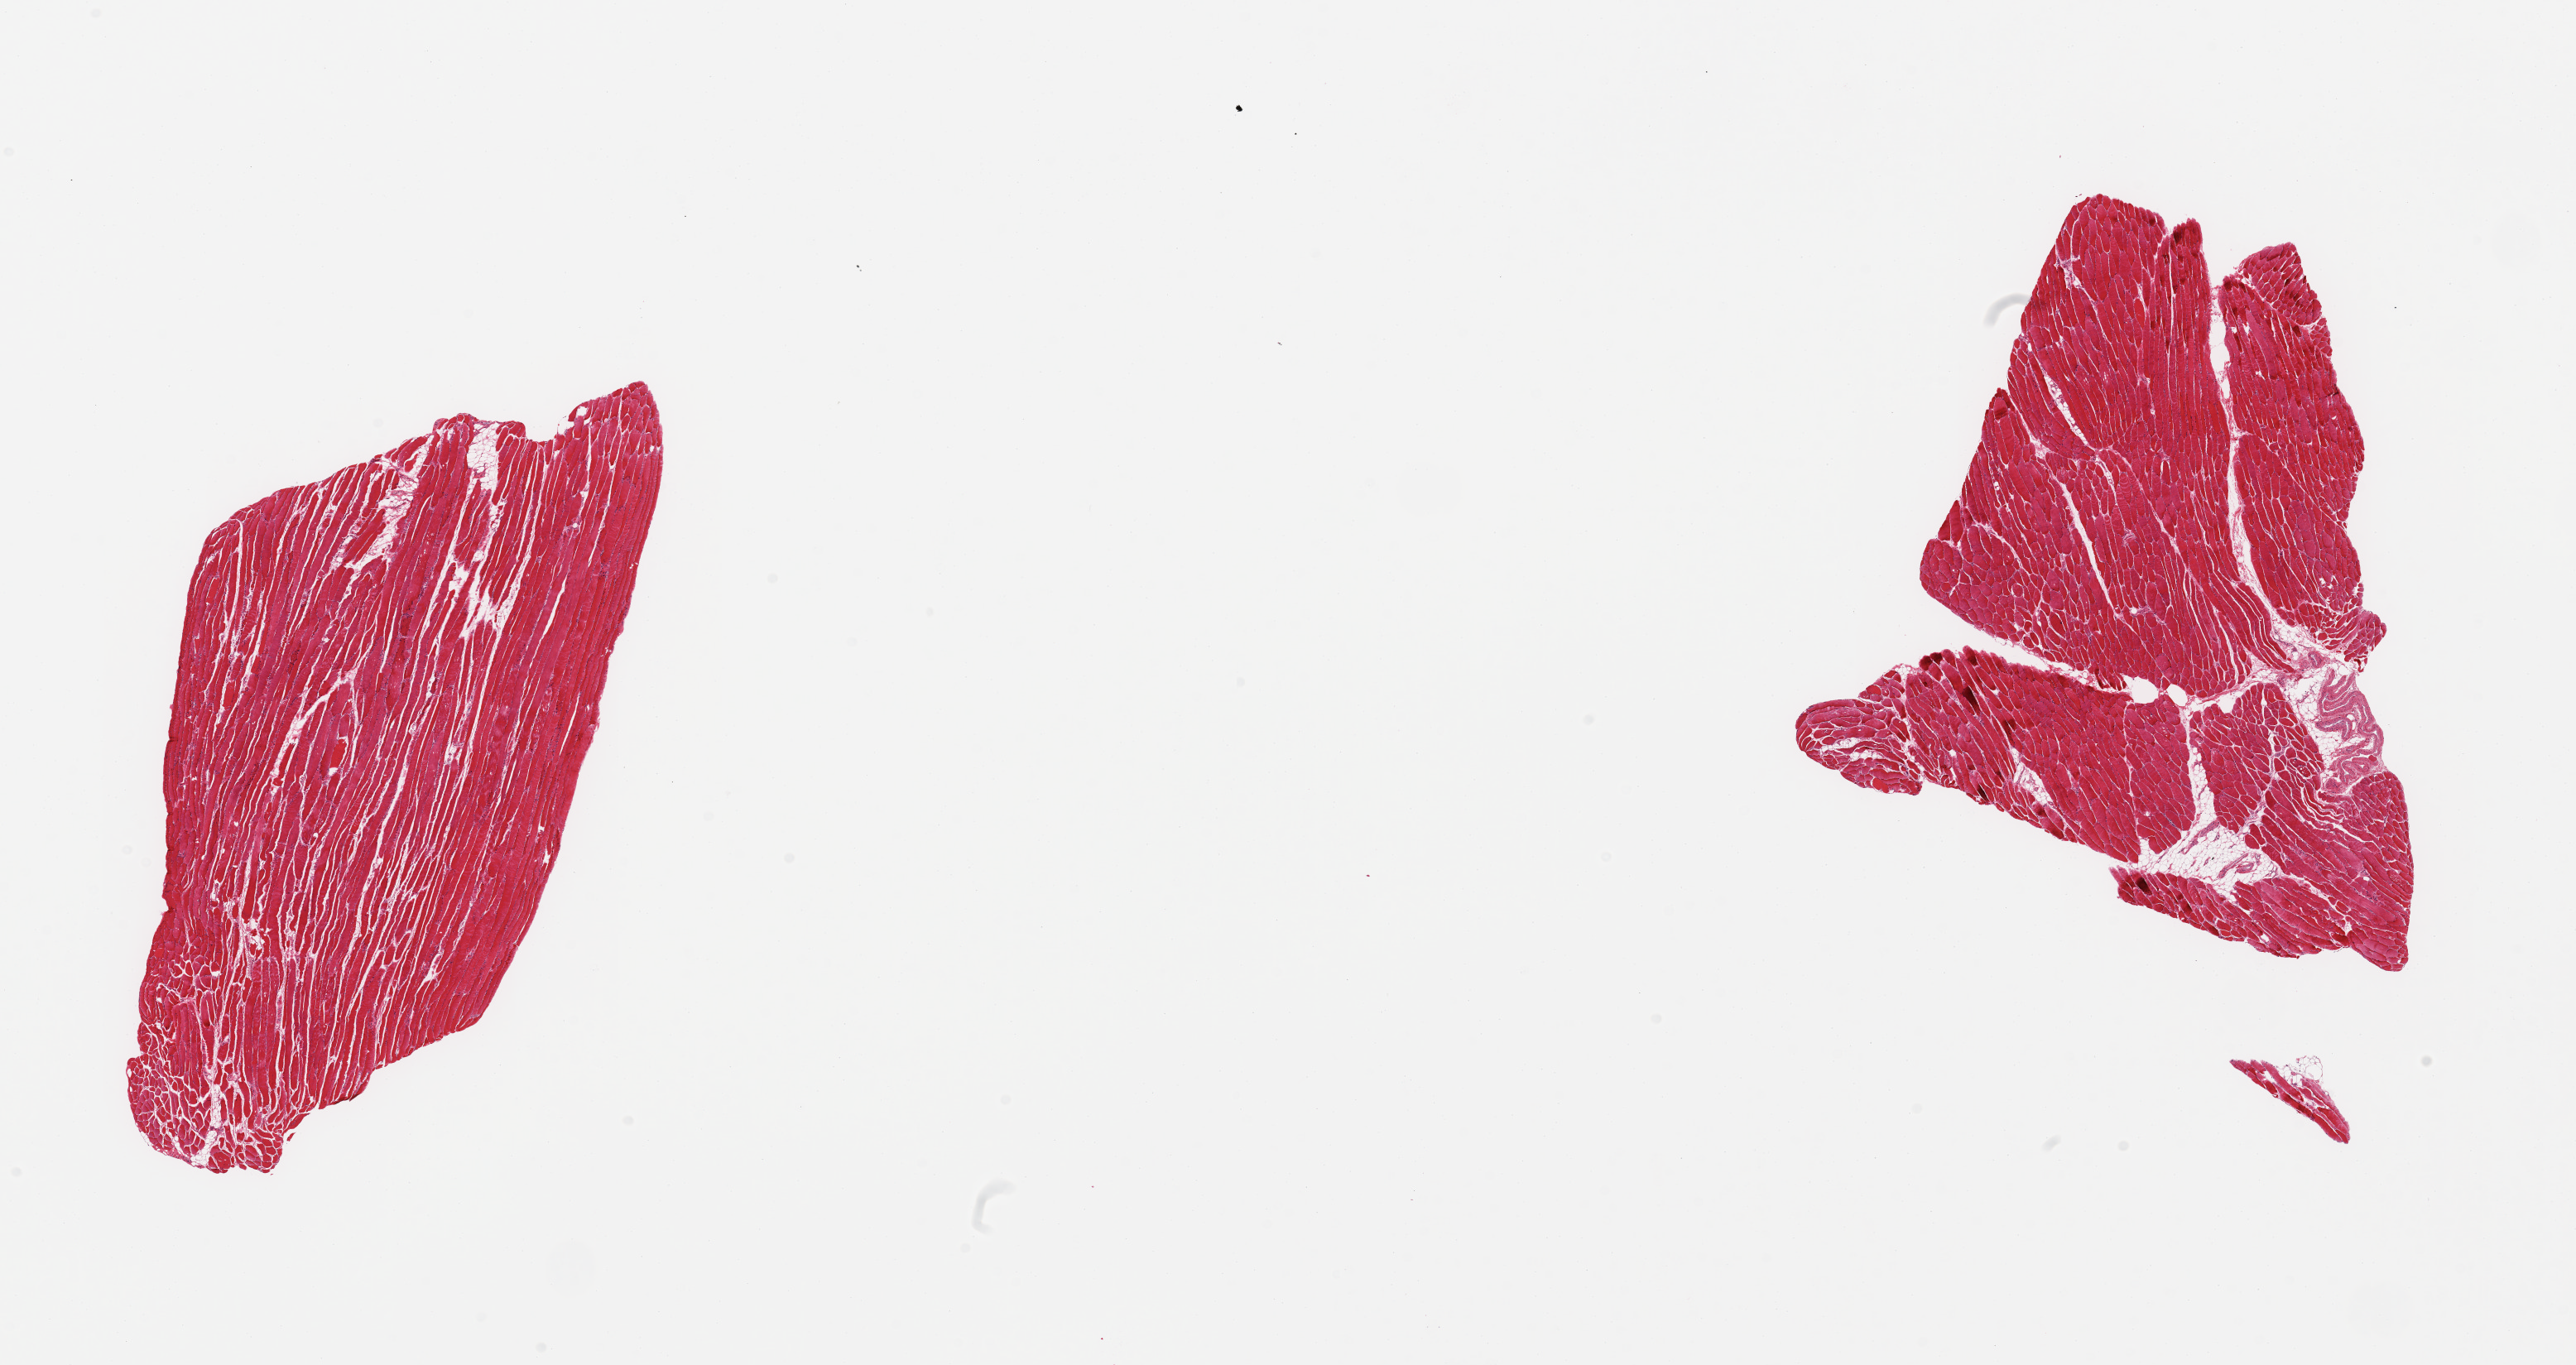
H&E whole-slide image — shown as a low-resolution overview of the whole scanned area (about 24.6 x 13.0 mm). PAXgene-fixed, paraffin-embedded tissue. Target tissue: skeletal muscle. Tissue donor sample.
Reviewer comment on this tissue sample: 2 pieces; 5% internal fat in 1 piece.